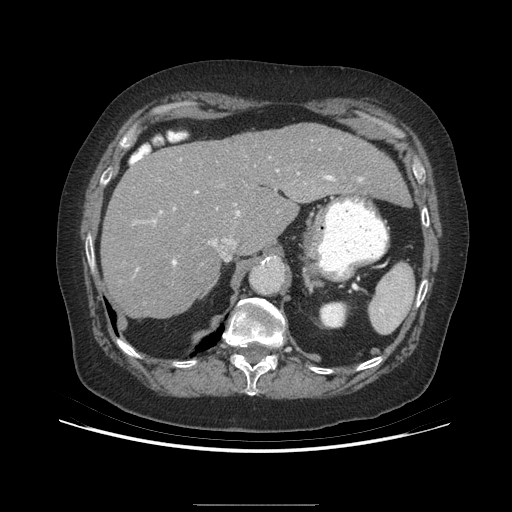
Contrast-enhanced abdominal CT (liver protocol), one axial slice; slice 164 of 192 in the series (ordered by position); reconstruction kernel STANDARD; soft-tissue window (W 400 / L 40 HU); 2.5 mm slice thickness; 512 × 512 image matrix, field of view 400 × 400 mm. From the clinical record (not read from this slice): diagnosis: hepatocellular carcinoma (patient treated with transarterial chemoembolisation; whether this scan precedes or follows treatment is not stated here); TNM stage (as recorded): Stage-I; Child-Pugh class: A; tumour size: 3.2 cm.
Outlined on this slice (semi-automatic segmentation, software-assisted and operator-edited):
- liver parenchyma outside the tumour (the mass and vessels are separate outlines, so this box may not span the whole liver): bounding box (x1, y1, x2, y2) in pixels: (100, 124, 408, 318)
- liver vessels: (137, 170, 363, 270)